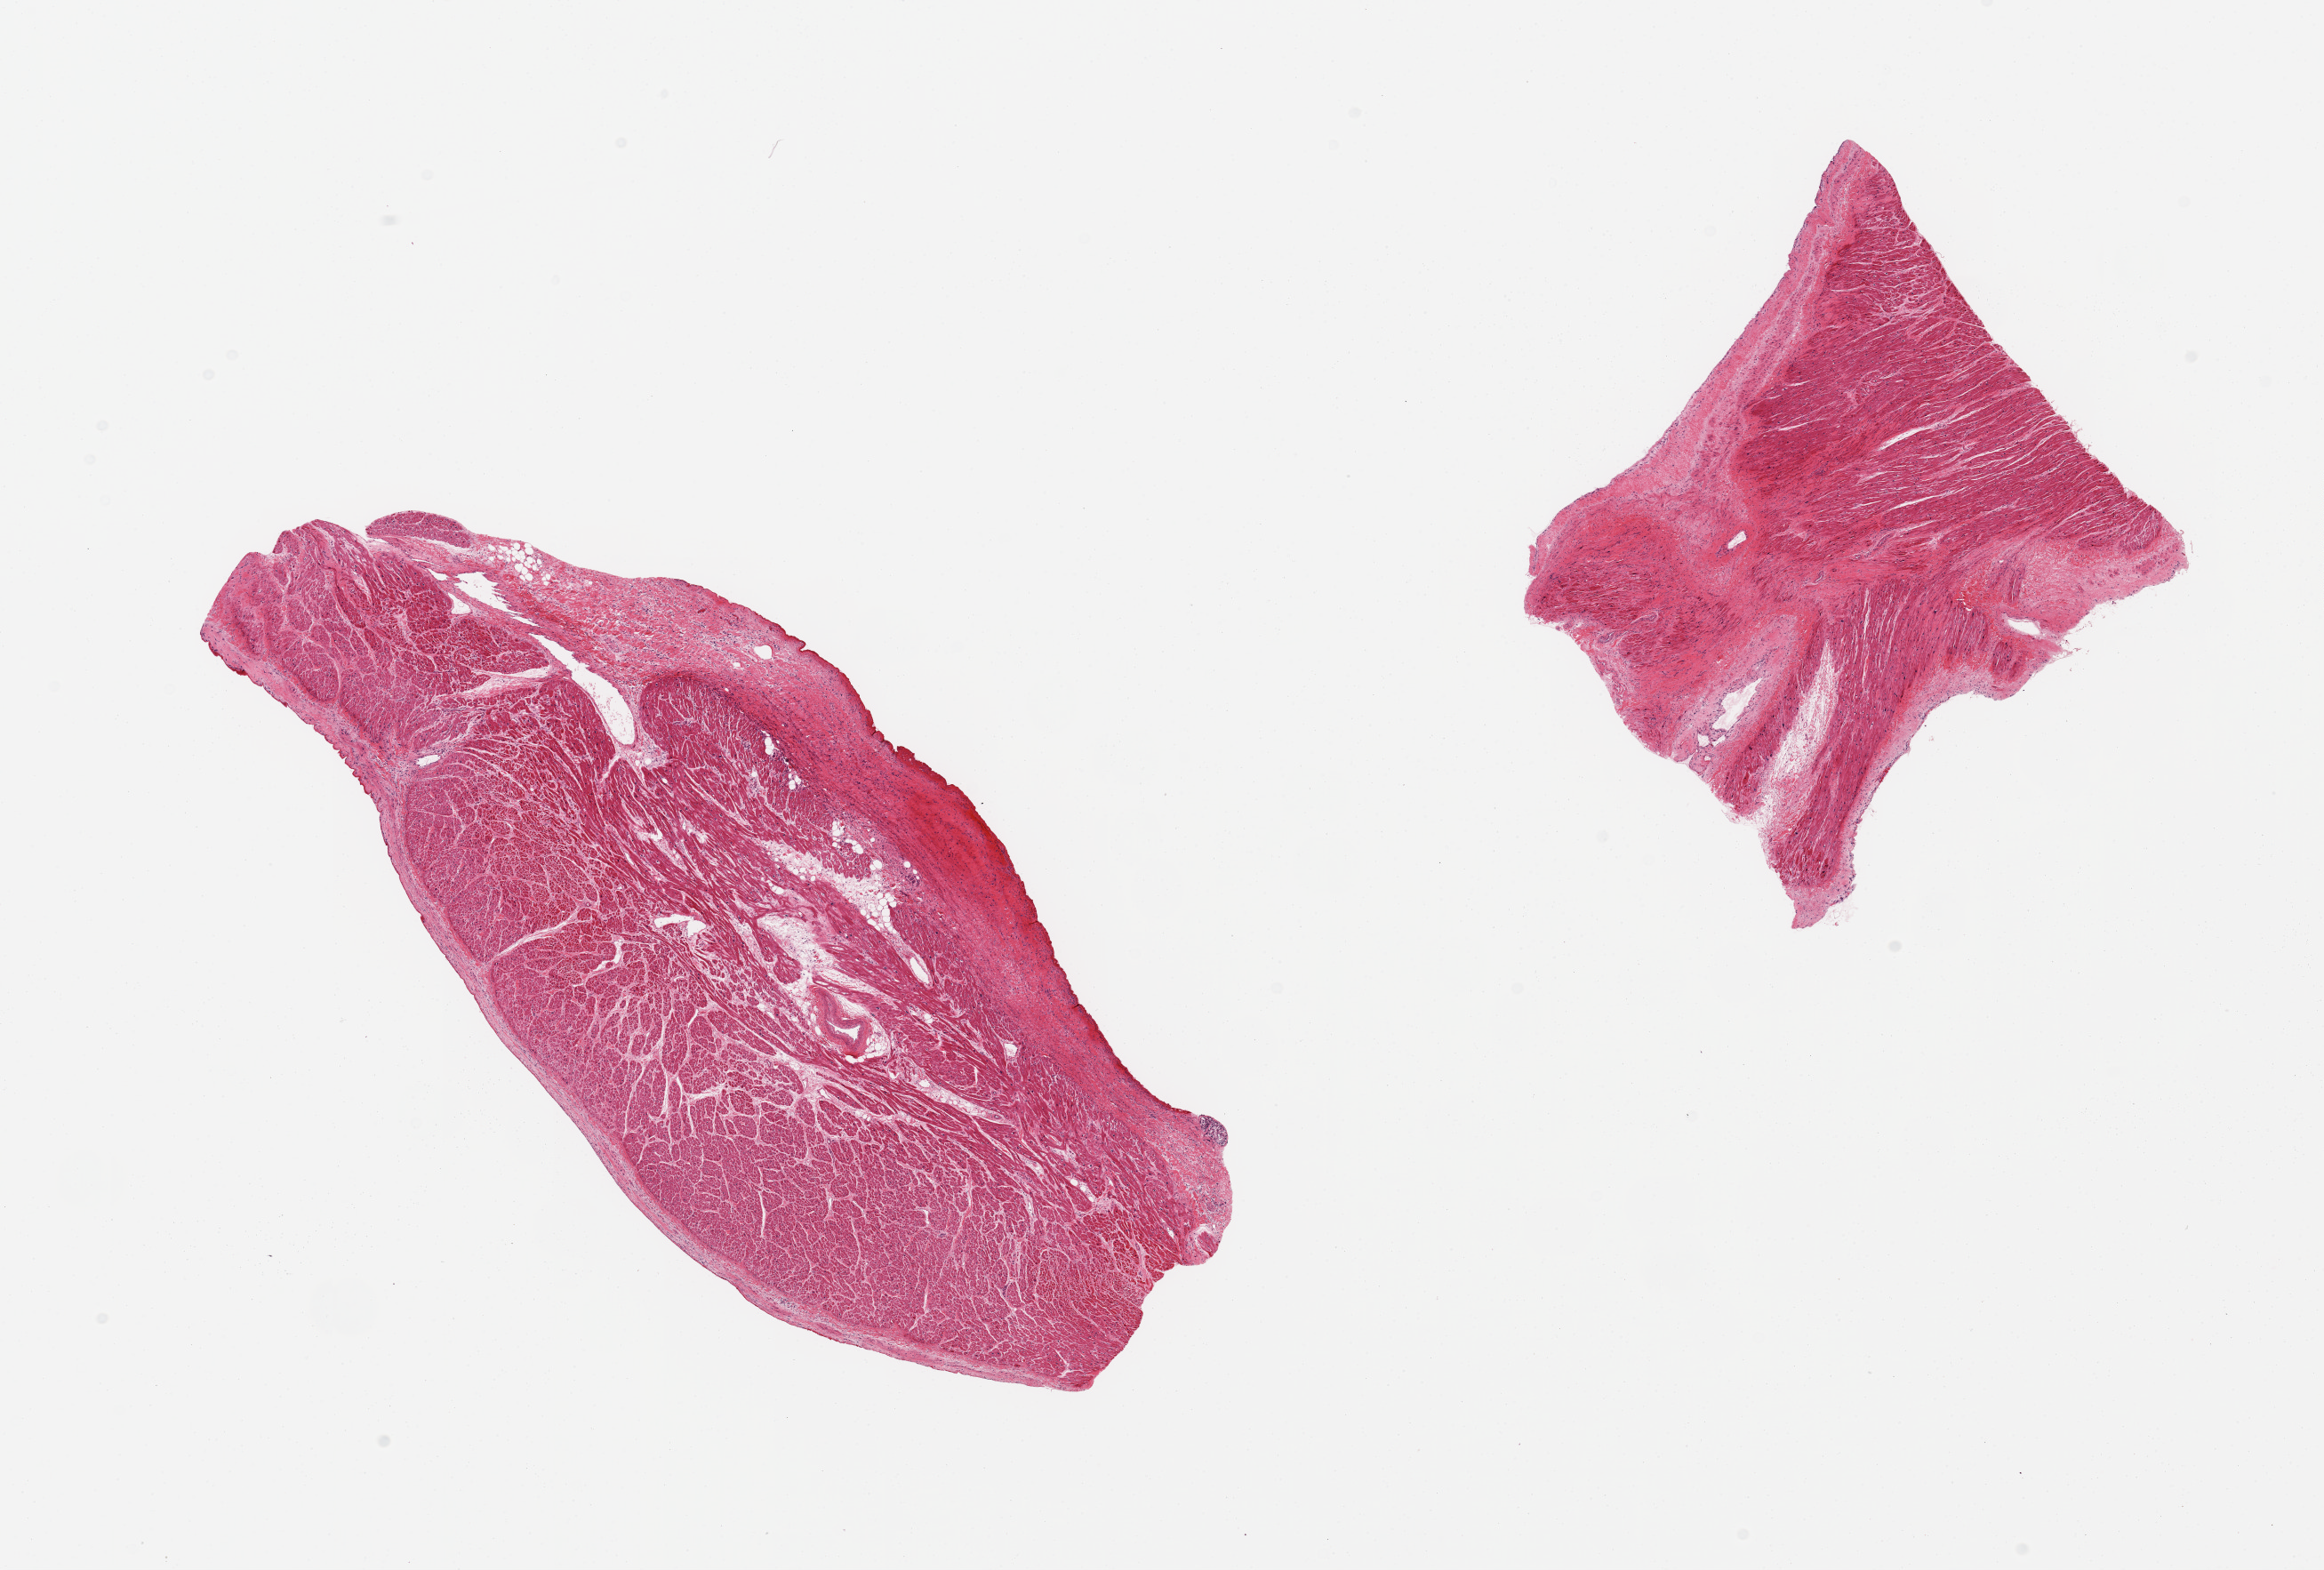
Digitized H&E-stained section — a low-resolution overview of the entire scanned area, about 20.7 x 14.0 mm (slide scanned at 20x). PAXgene-fixed, paraffin-embedded tissue. Section of auricular appendage (target tissue). Donor tissue sample.
- pathologist's review note for this sample: 2 pieces; 20 & 30% fibrous content